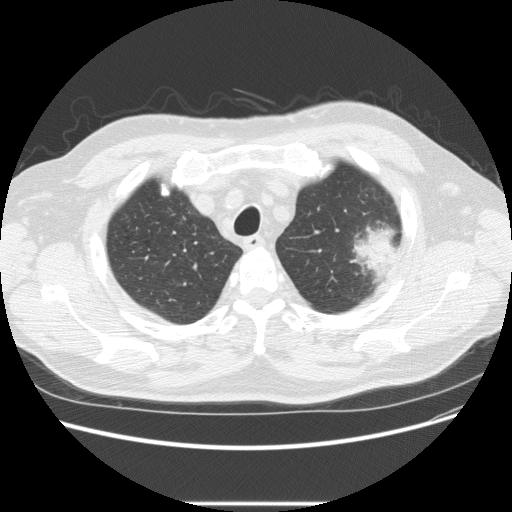
Low-dose screening chest CT, one axial slice. Position 190 of 233 along the scan axis. Reconstruction kernel STANDARD. 120 kVp. Lung window (W 1500 / L -600 HU). 512 × 512 image matrix, field of view 380 × 380 mm.
Outlined on this slice (outlined manually by an expert reader):
- lesion 1 (tumor, upper lobe of left lung): bounding box (x1, y1, x2, y2) in pixels: (351, 224, 402, 280)